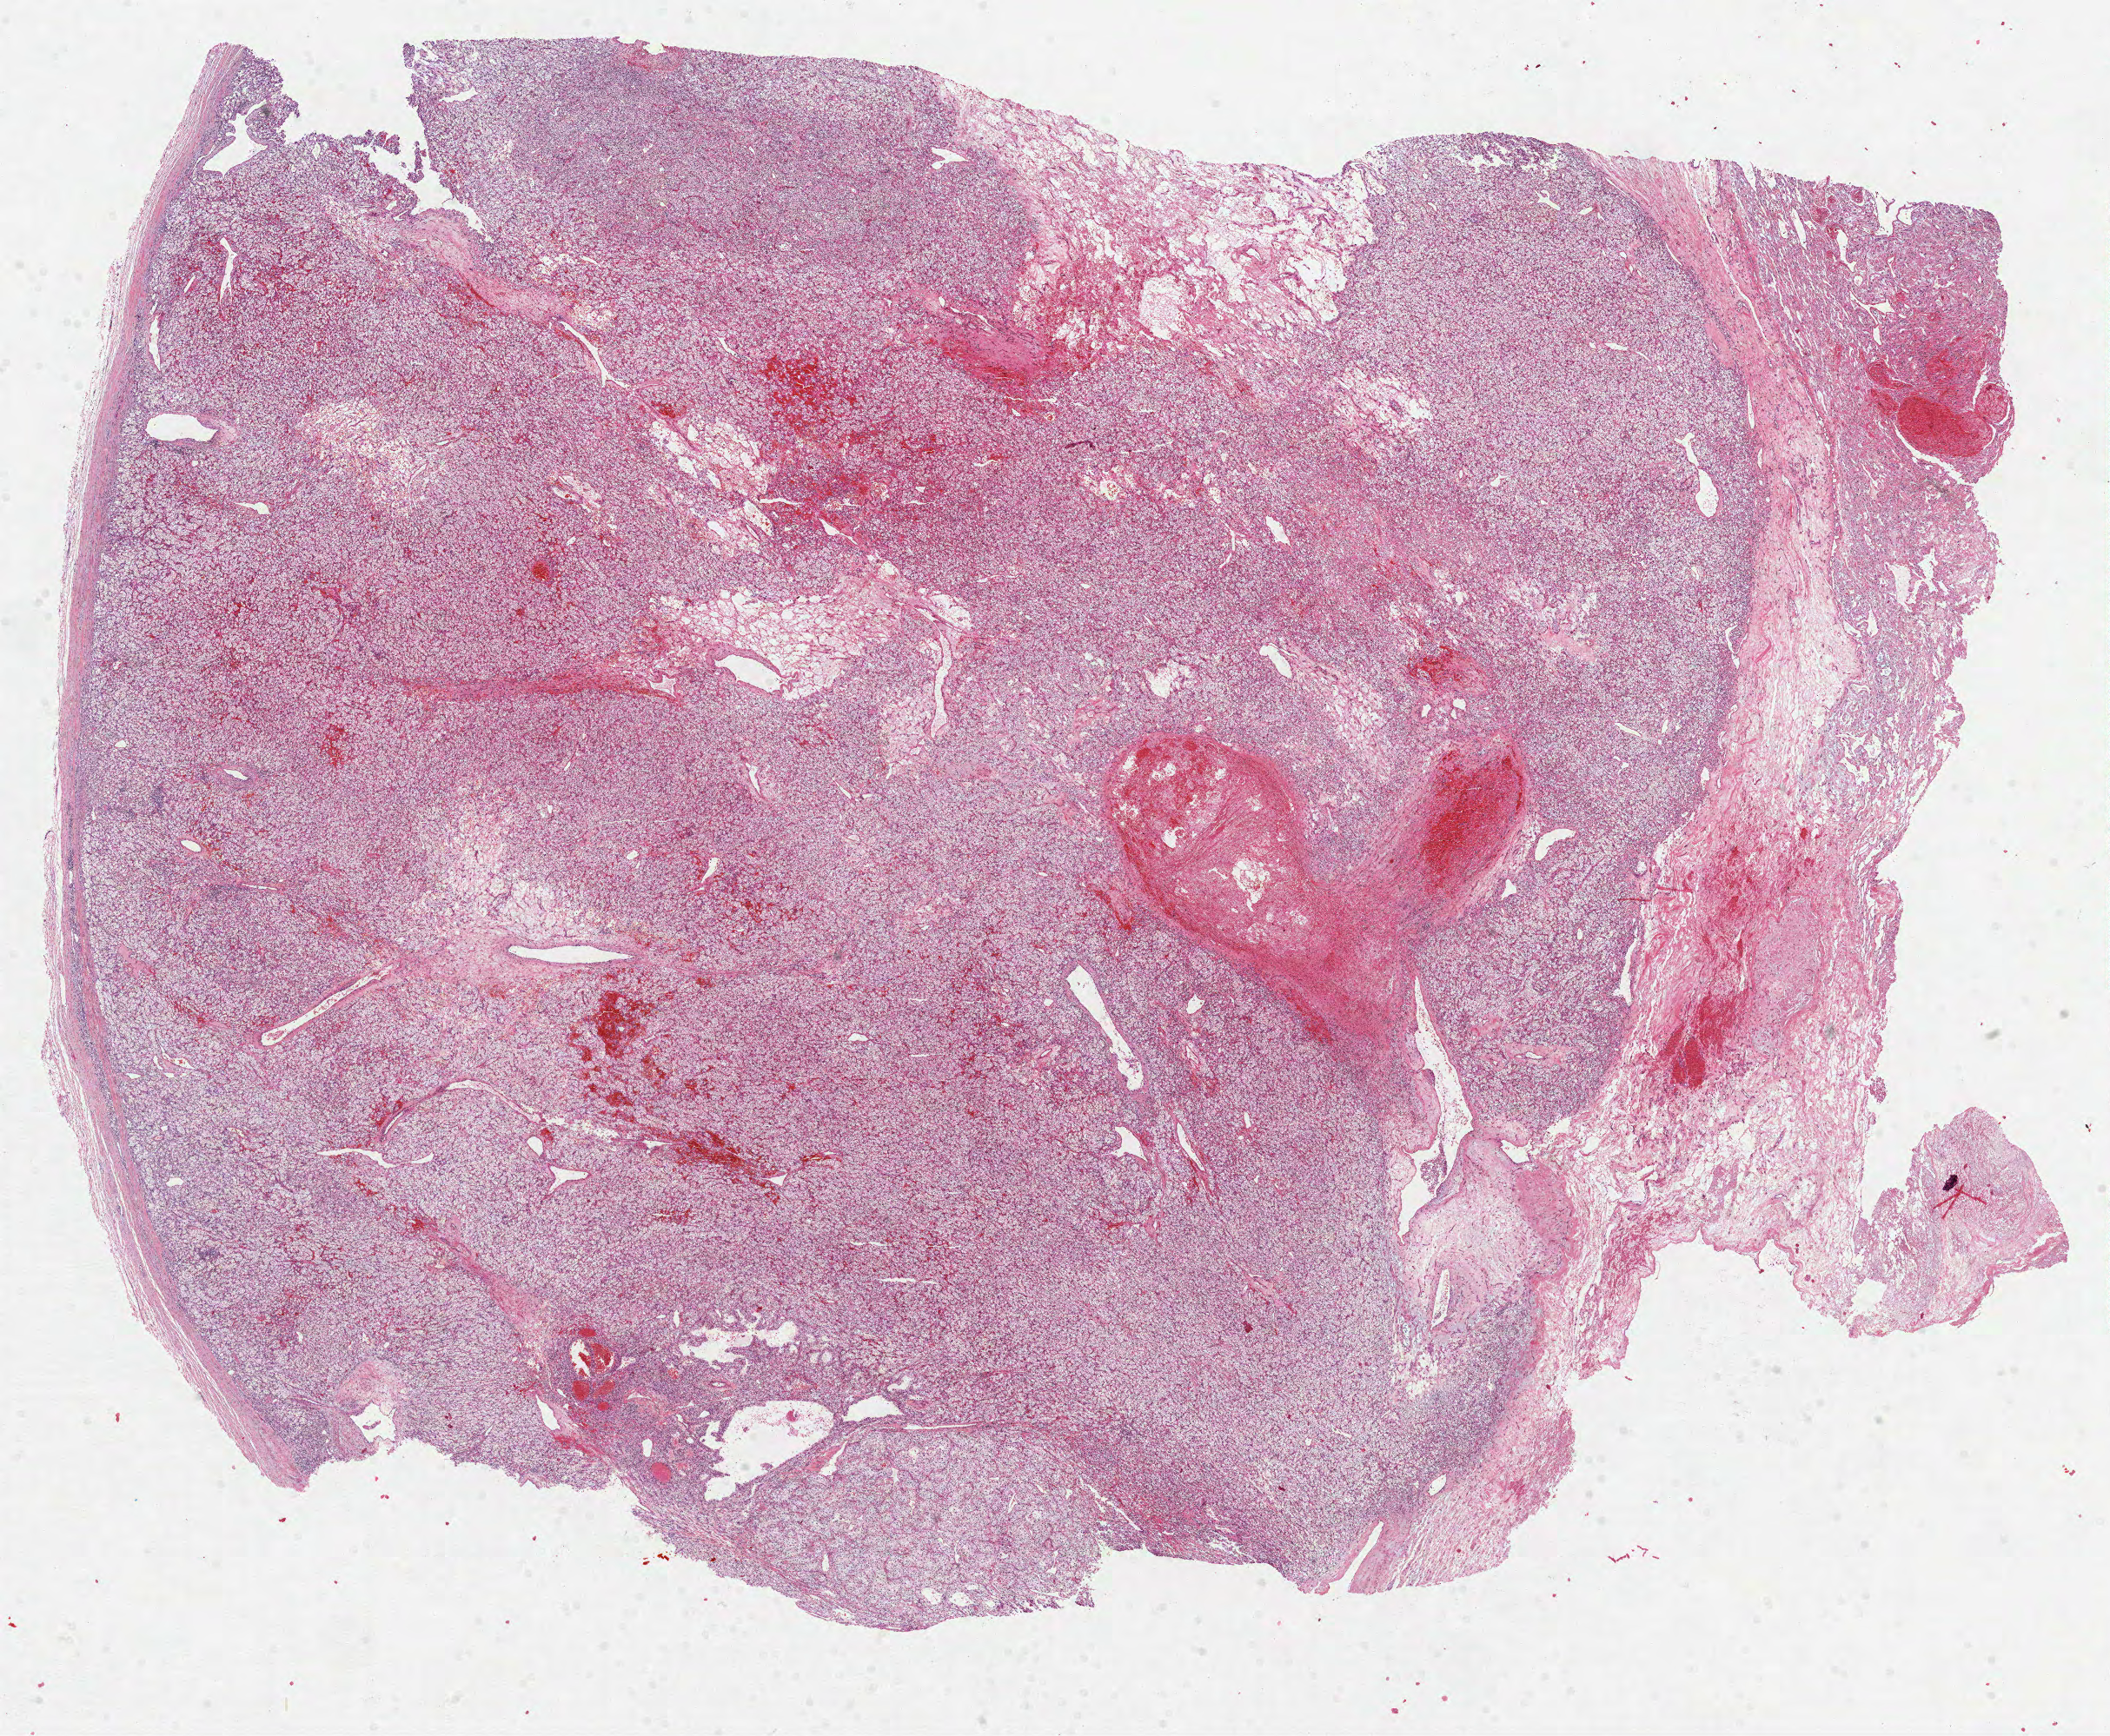
Digitized H&E-stained tissue section (whole slide) — whole scanned area (about 19.6 x 16.1 mm, from a 40x scan) shown as a low-resolution overview; FFPE section; kidney, primary tumour sample. Patient: female, age at initial diagnosis 78 years. Histologic grade: G2 (moderately differentiated).
- TNM: T2 N0 M0
- AJCC pathologic stage: II
- histologic diagnosis: Clear cell adenocarcinoma, NOS